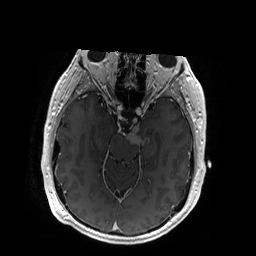
Brain MRI from a brain-tumour surgery series, one axial slice. Slice 119 of 192 in the series (ordered by position). T1-weighted post-contrast. 1 mm slice thickness. 256 × 256 image matrix, field of view 256 × 256 mm. Case-level facts recorded for this patient, not image findings: histopathology: Glioblastoma; WHO grade: 4; IDH mutation: no.
Structures marked on this image (expert manual segmentation):
- tumour: bounding box <126,126,142,144> (left, top, right, bottom; pixels)